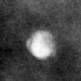
Cropped region of a digitized screen-film mammogram centred on a radiologist-marked abnormality, left breast, MLO view, BI-RADS breast density category 2 (scale 1–4).
Marked abnormality: calcifications, morphology coarse / round and regular / lucent center; BI-RADS assessment category 2; subtlety rating 4 on a 1 (subtle) to 5 (obvious) scale; benign without callback (not worked up further).